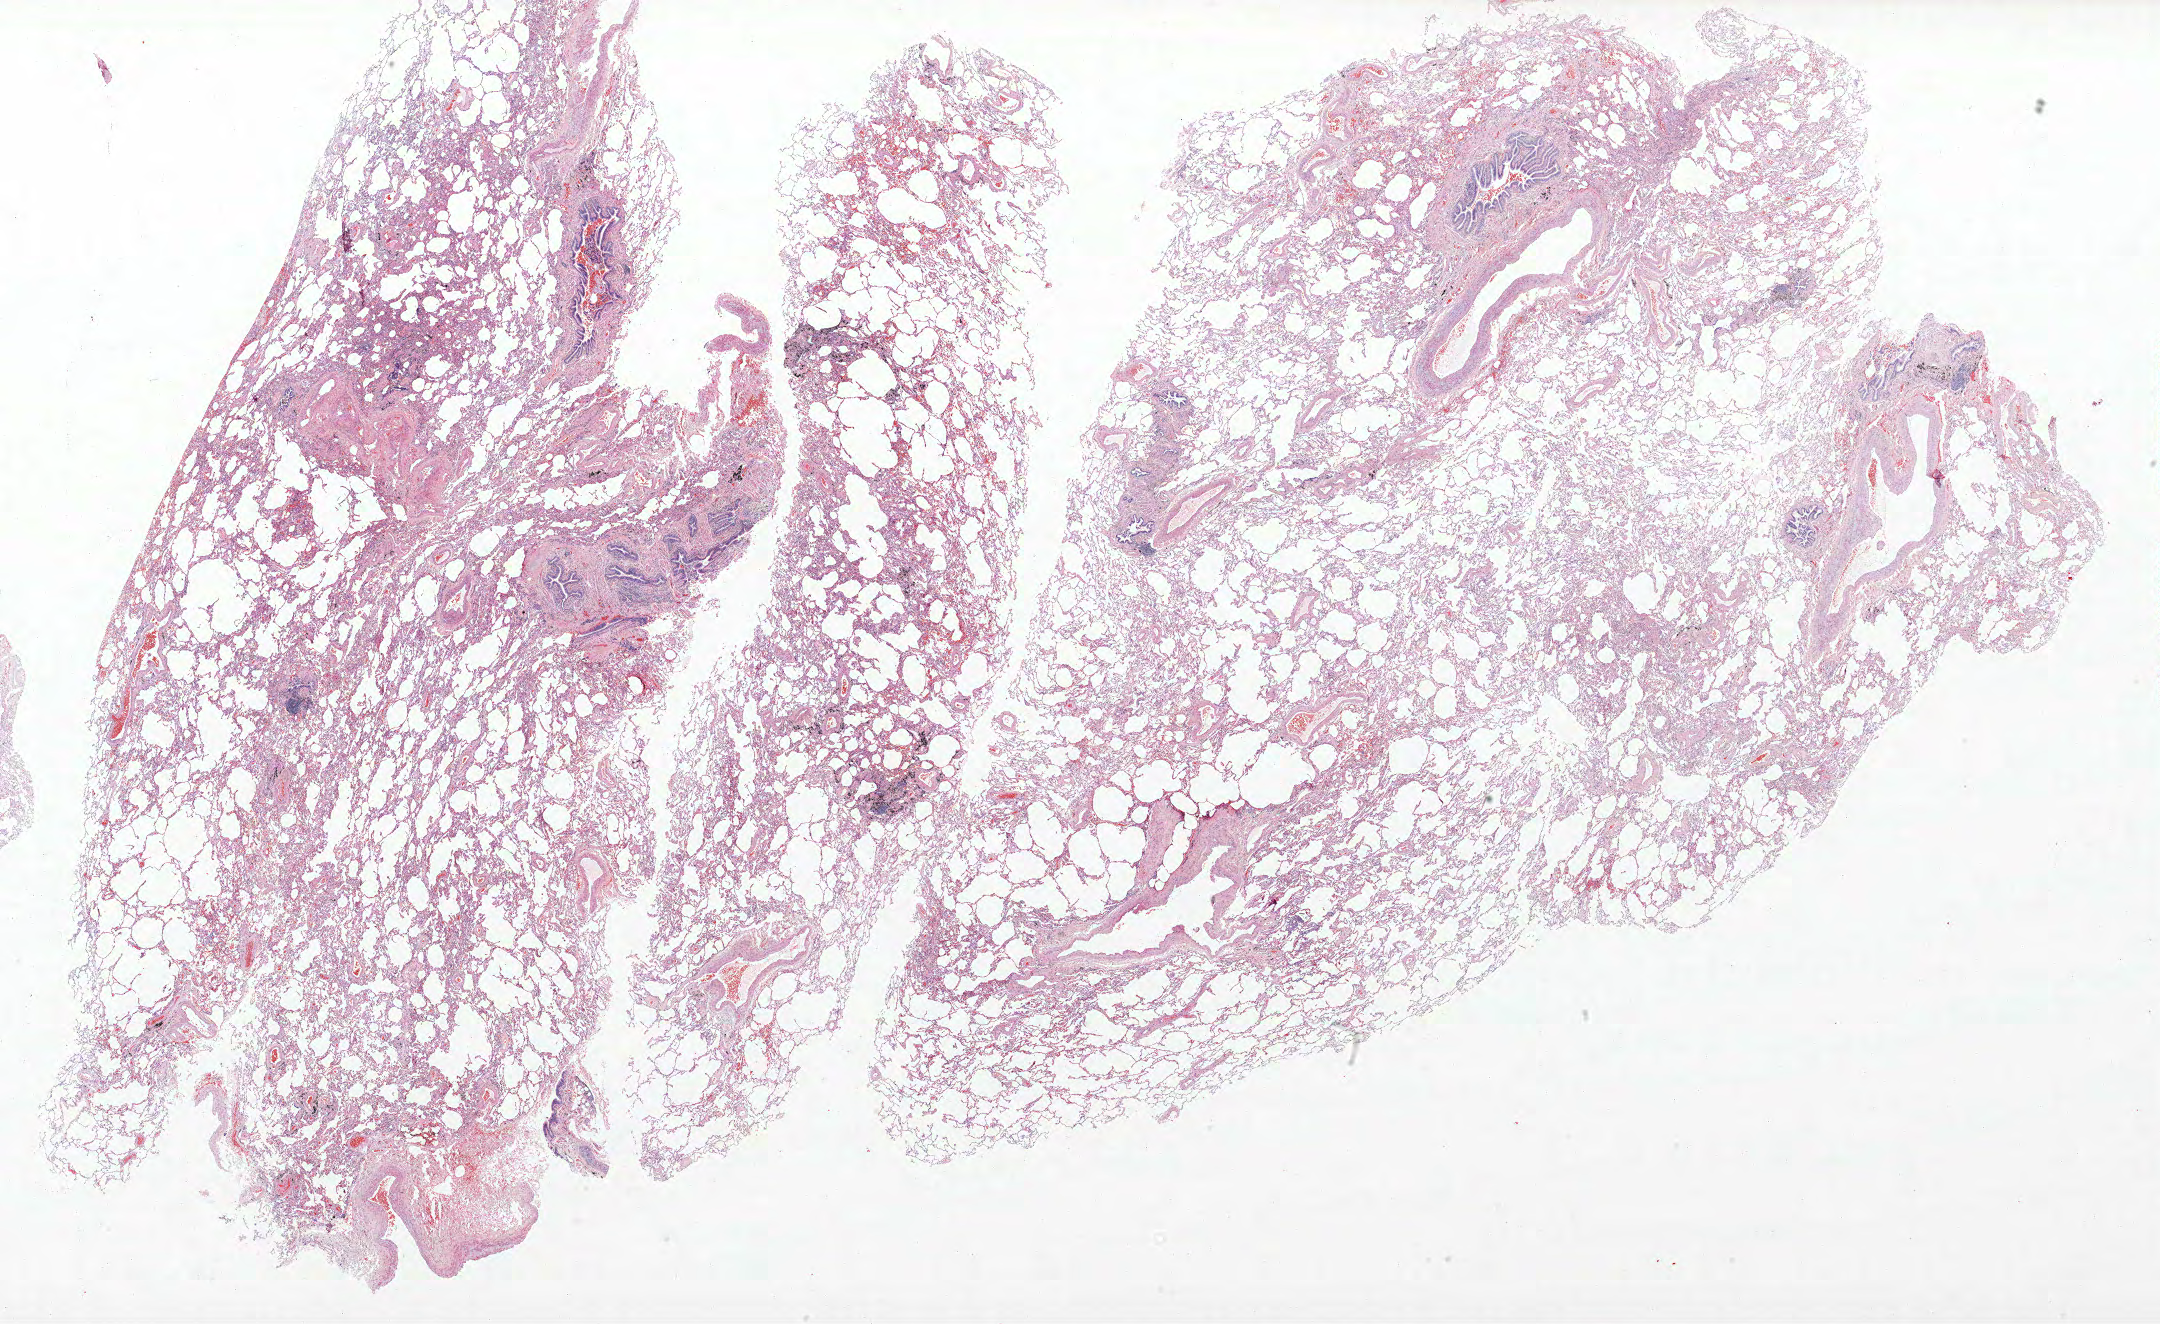
H&E whole-slide image — low-resolution overview of the scanned area, about 34.6 x 21.2 mm (from a 40x scan), formalin-fixed paraffin-embedded (FFPE) section, lung. Male, age 74 at enrolment. Former smoker at enrolment. Grade: well differentiated (G1).
- participant's lung-cancer diagnosis: Papillary adenocarcinoma, NOS
- primary tumour location (clinical record): right middle lobe
- tumour size (pathology): 20 mm
- stage (AJCC 6th edition): IA